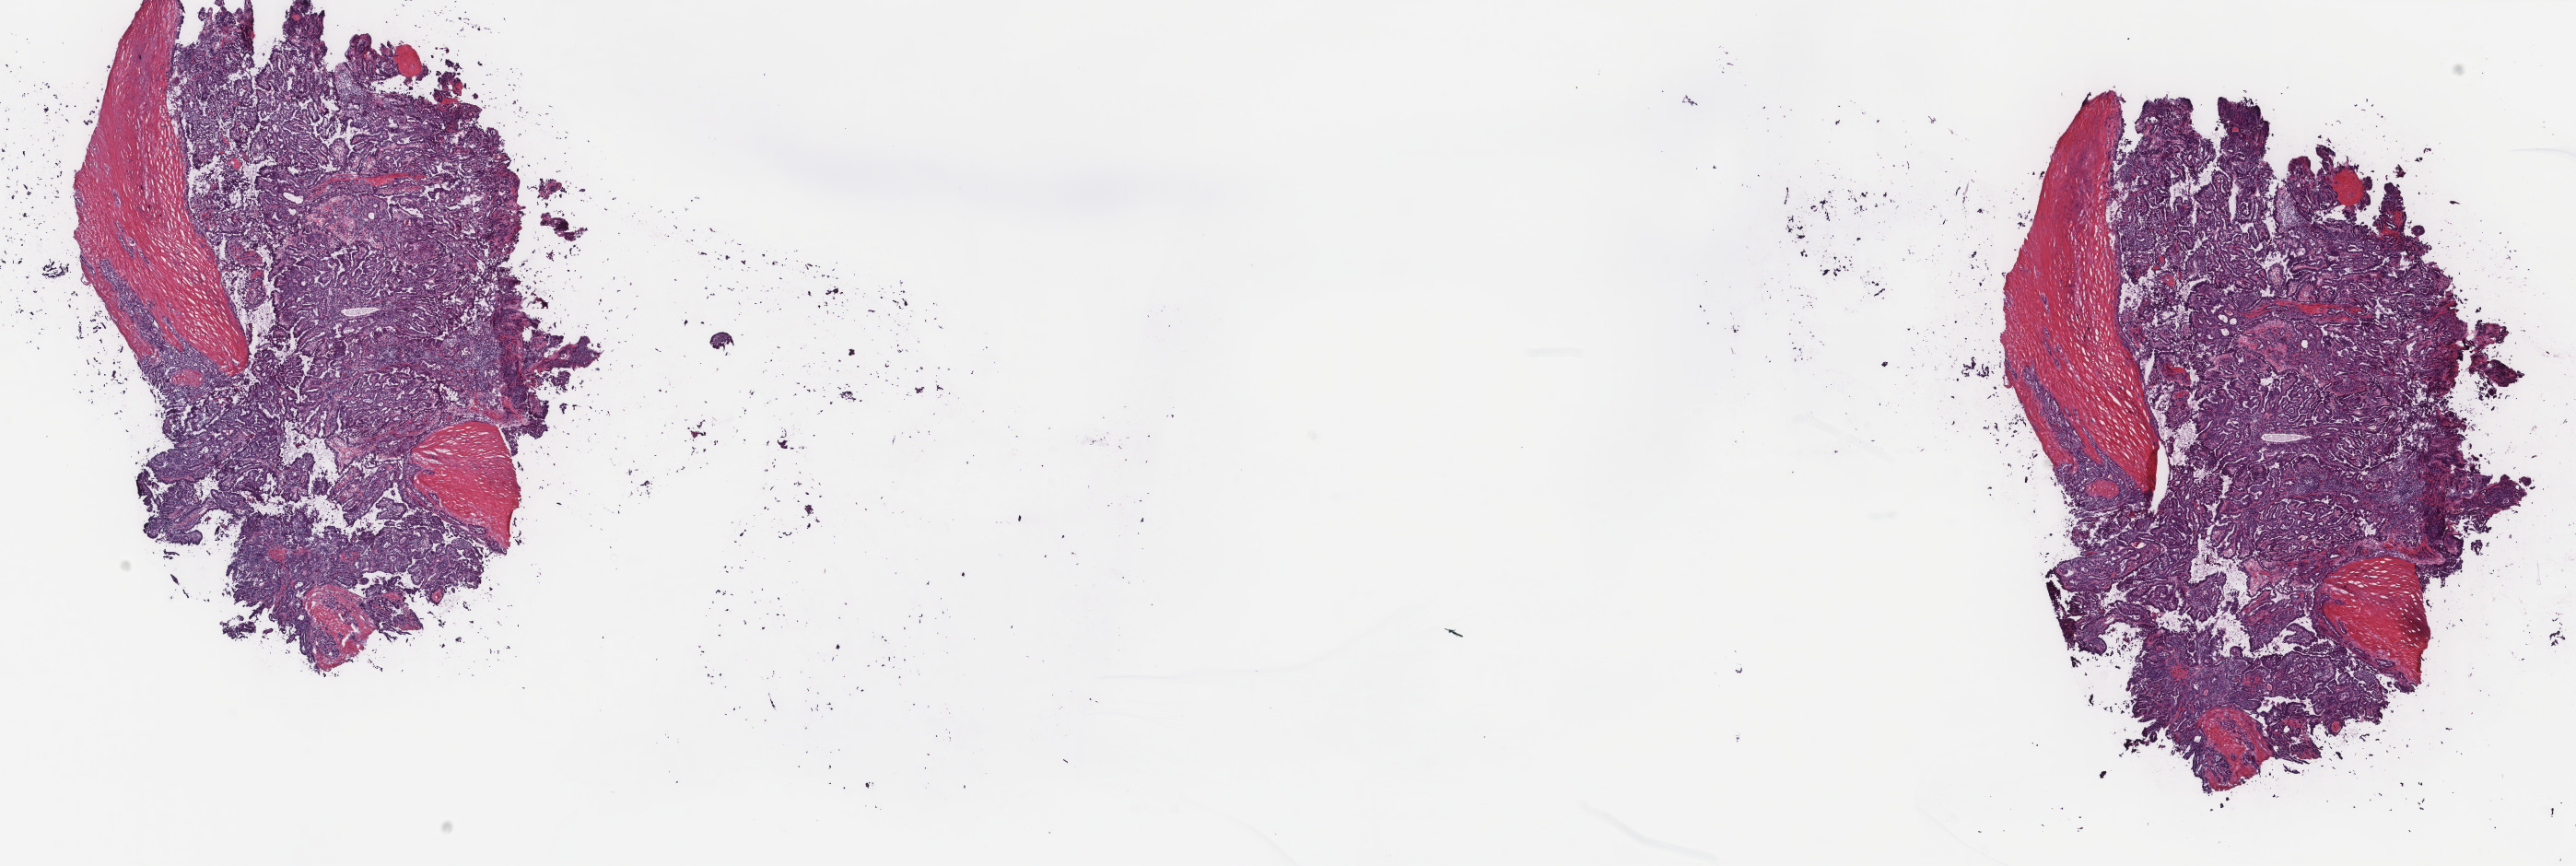
Whole-slide histology image, Hematoxylin and eosin (H&E) stained — whole scanned area (about 22.2 x 7.5 mm) shown as a low-resolution overview; frozen section from the top of the tissue portion; sample: primary tumour, thyroid. Female patient; age at initial diagnosis 42 years. Composition of this section per pathologist review: tumour cells 85%, tumour nuclei 80%, normal cells 0%, stromal cells 15%, necrosis 0%. Infiltration values recorded for this section: lymphocyte infiltration 15%, monocyte infiltration 20%, neutrophil infiltration 0%.
AJCC pathologic stage: I. Lymph nodes positive (case pathology): 0 of 4 examined. Laterality: right. Pathologic diagnosis: Papillary adenocarcinoma, NOS (thyroid gland).